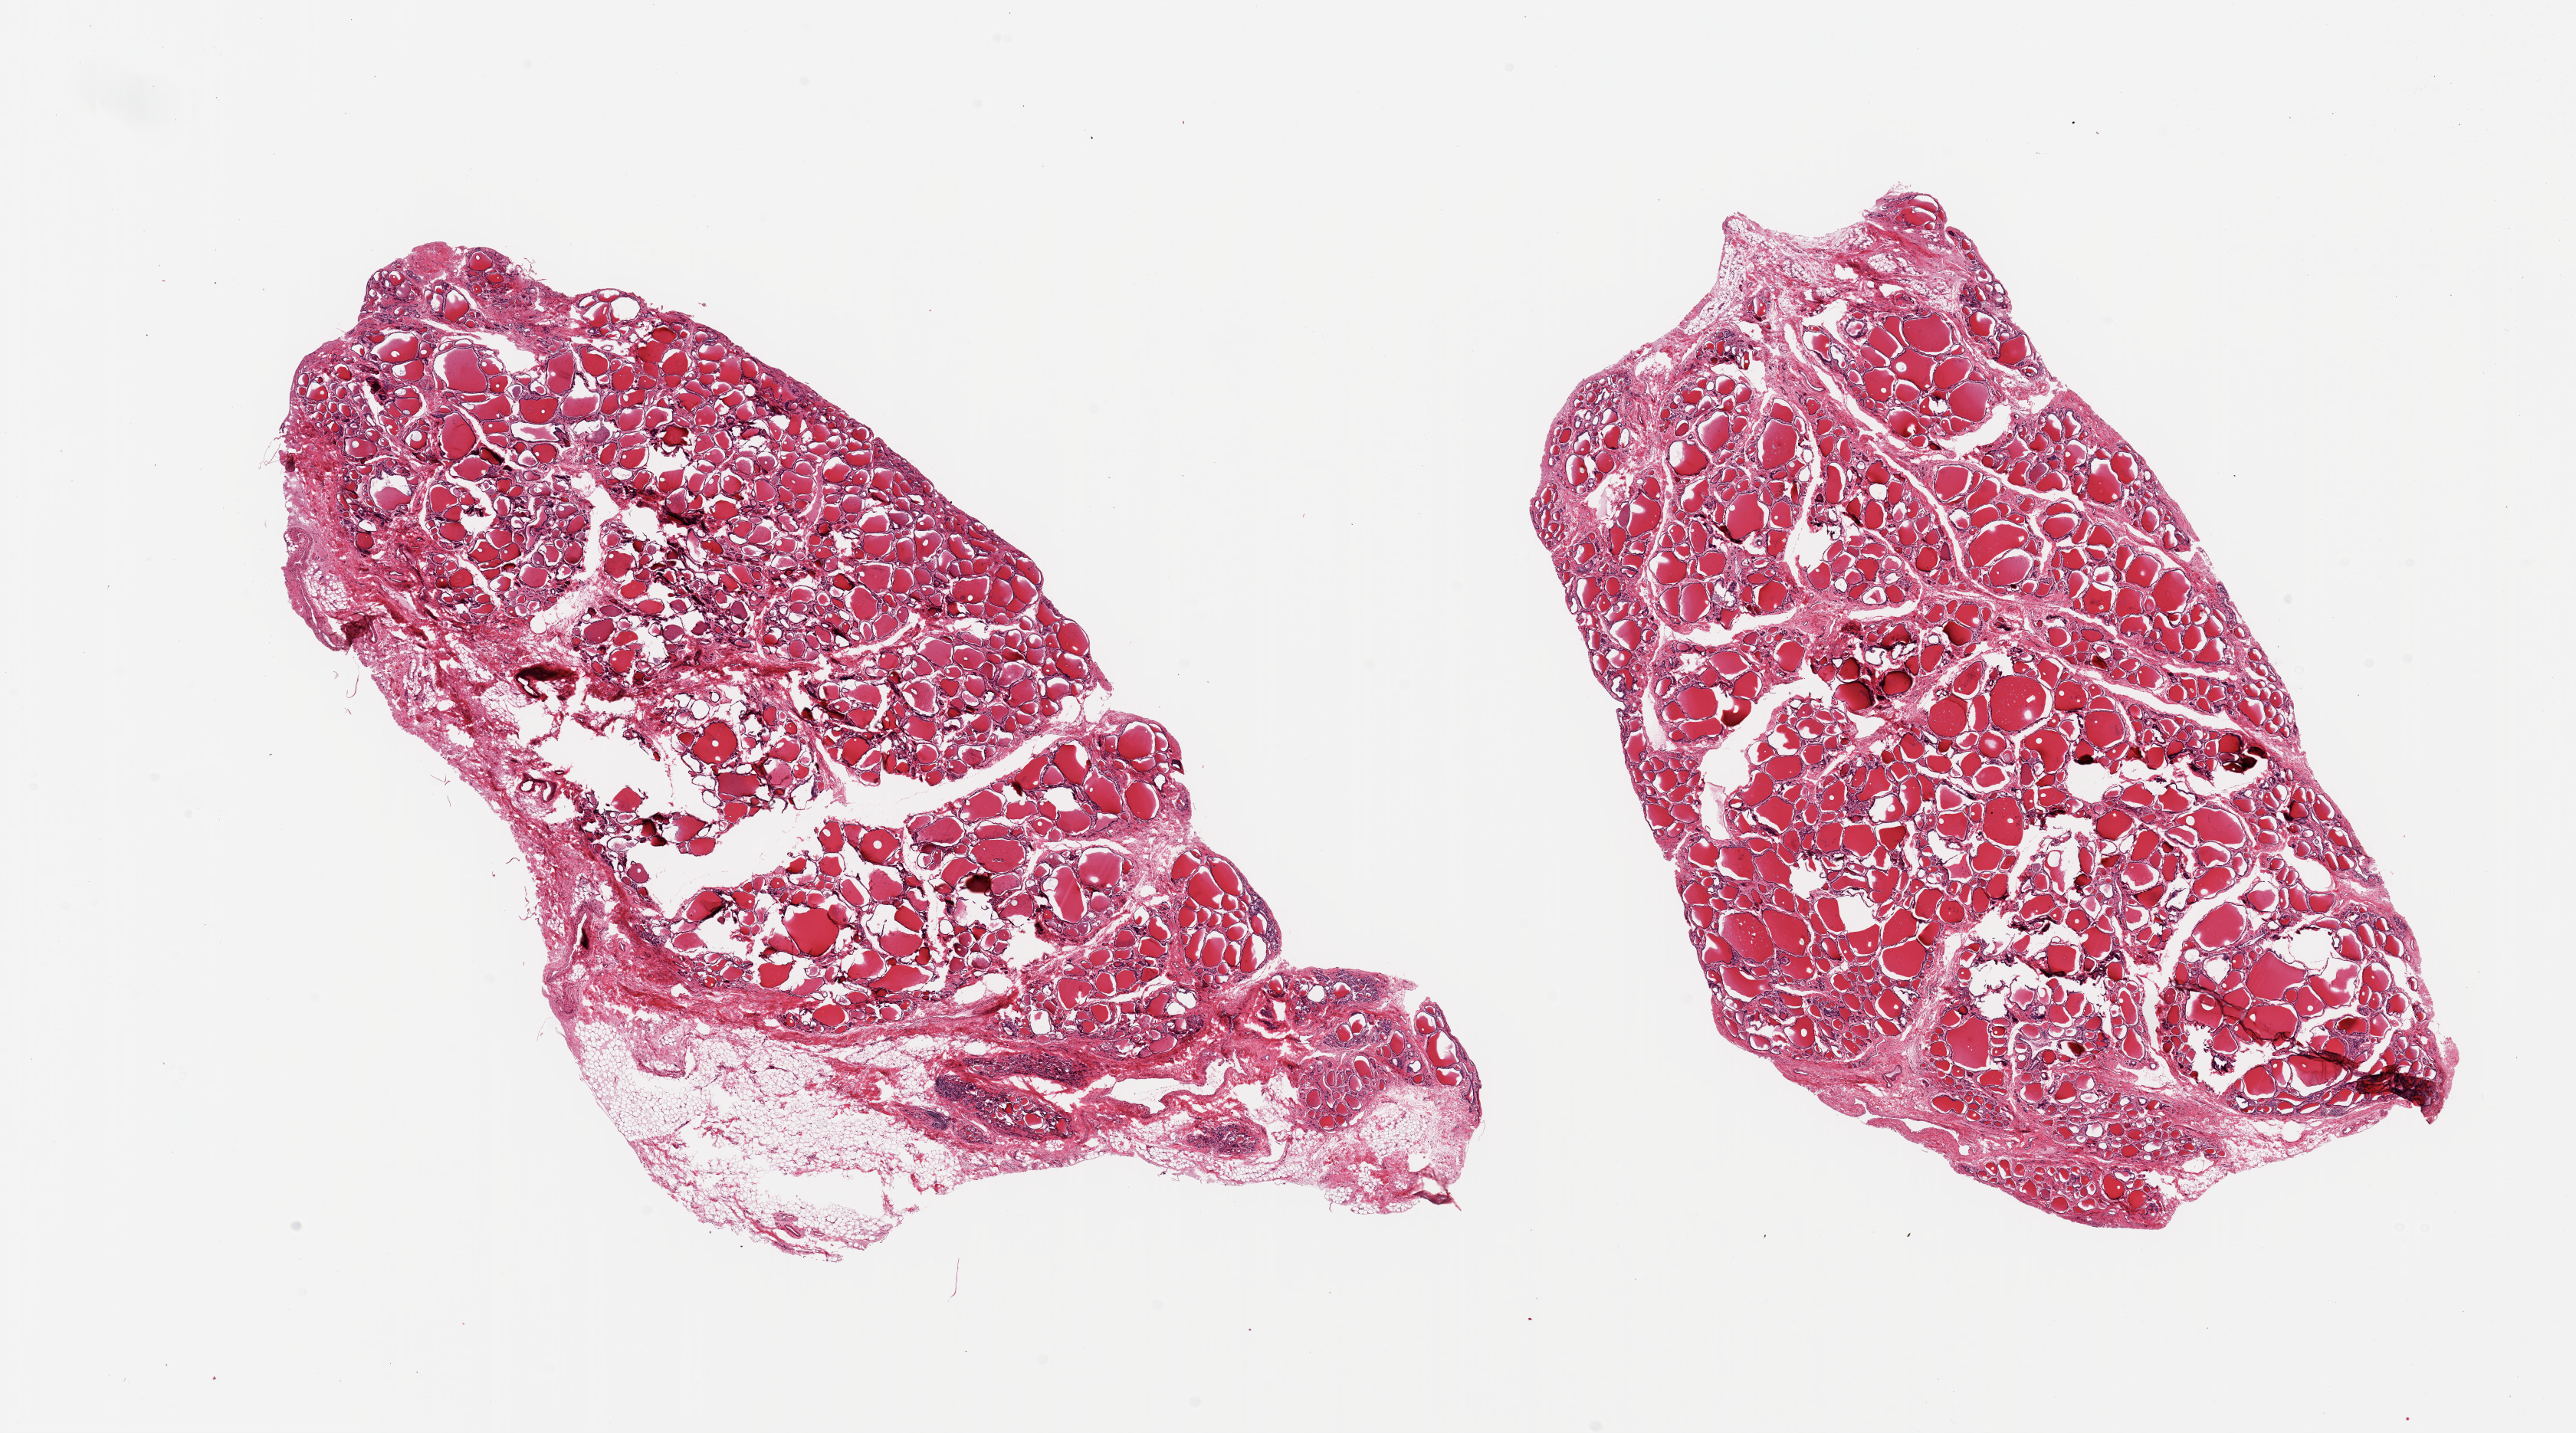
H&E whole-slide image, brightfield — whole scanned area (about 26.6 x 14.8 mm) shown as a low-resolution overview. PAXgene-fixed paraffin-embedded (PFPE) section. Section of thyroid (target tissue). Tissue donor sample. Donor sex: male.
Pathologist's review note for this sample: 2 pieces, no abnormalities, ~2mm nubbin of fat on one edge.